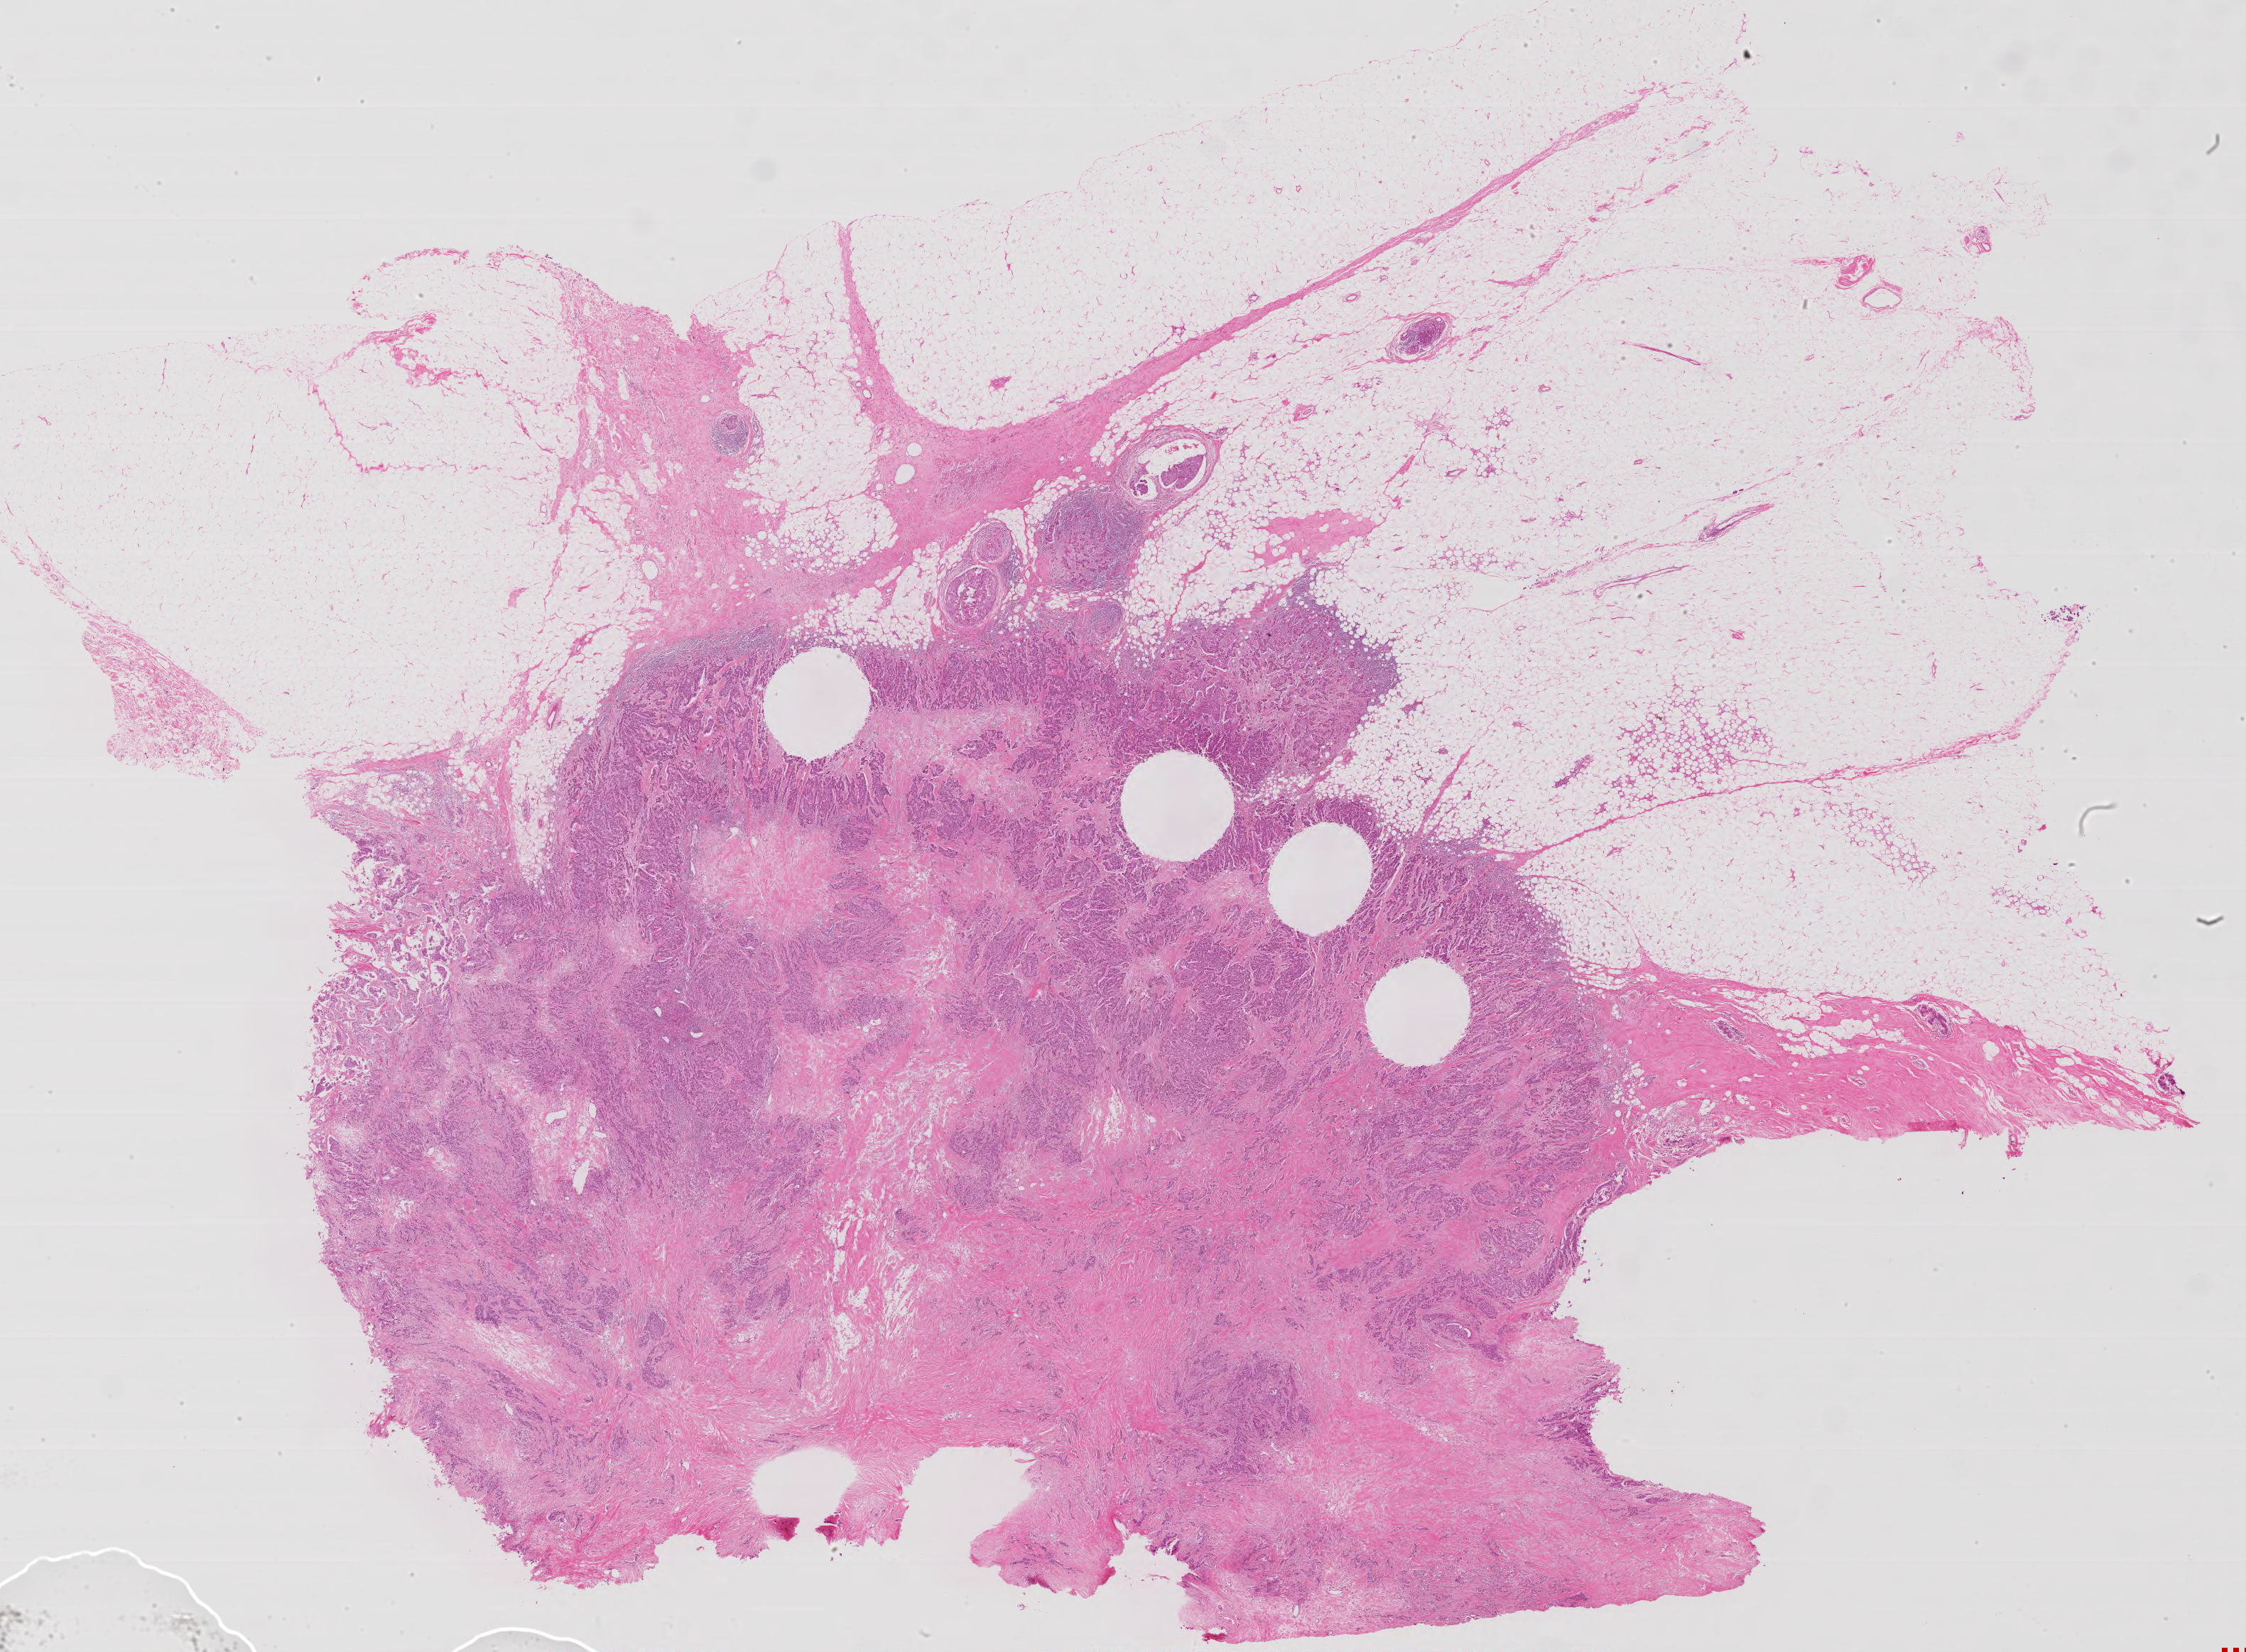
Digitized H&E-stained tissue section (whole slide), a low-resolution overview of the entire scanned area, about 25.3 x 18.6 mm (slide scanned at 40x). Formalin-fixed paraffin-embedded (FFPE) diagnostic section. Sample: primary tumour, breast. Female, age 50 years at initial diagnosis.
* AJCC pathologic stage: IIB
* histologic diagnosis: Infiltrating duct carcinoma, NOS